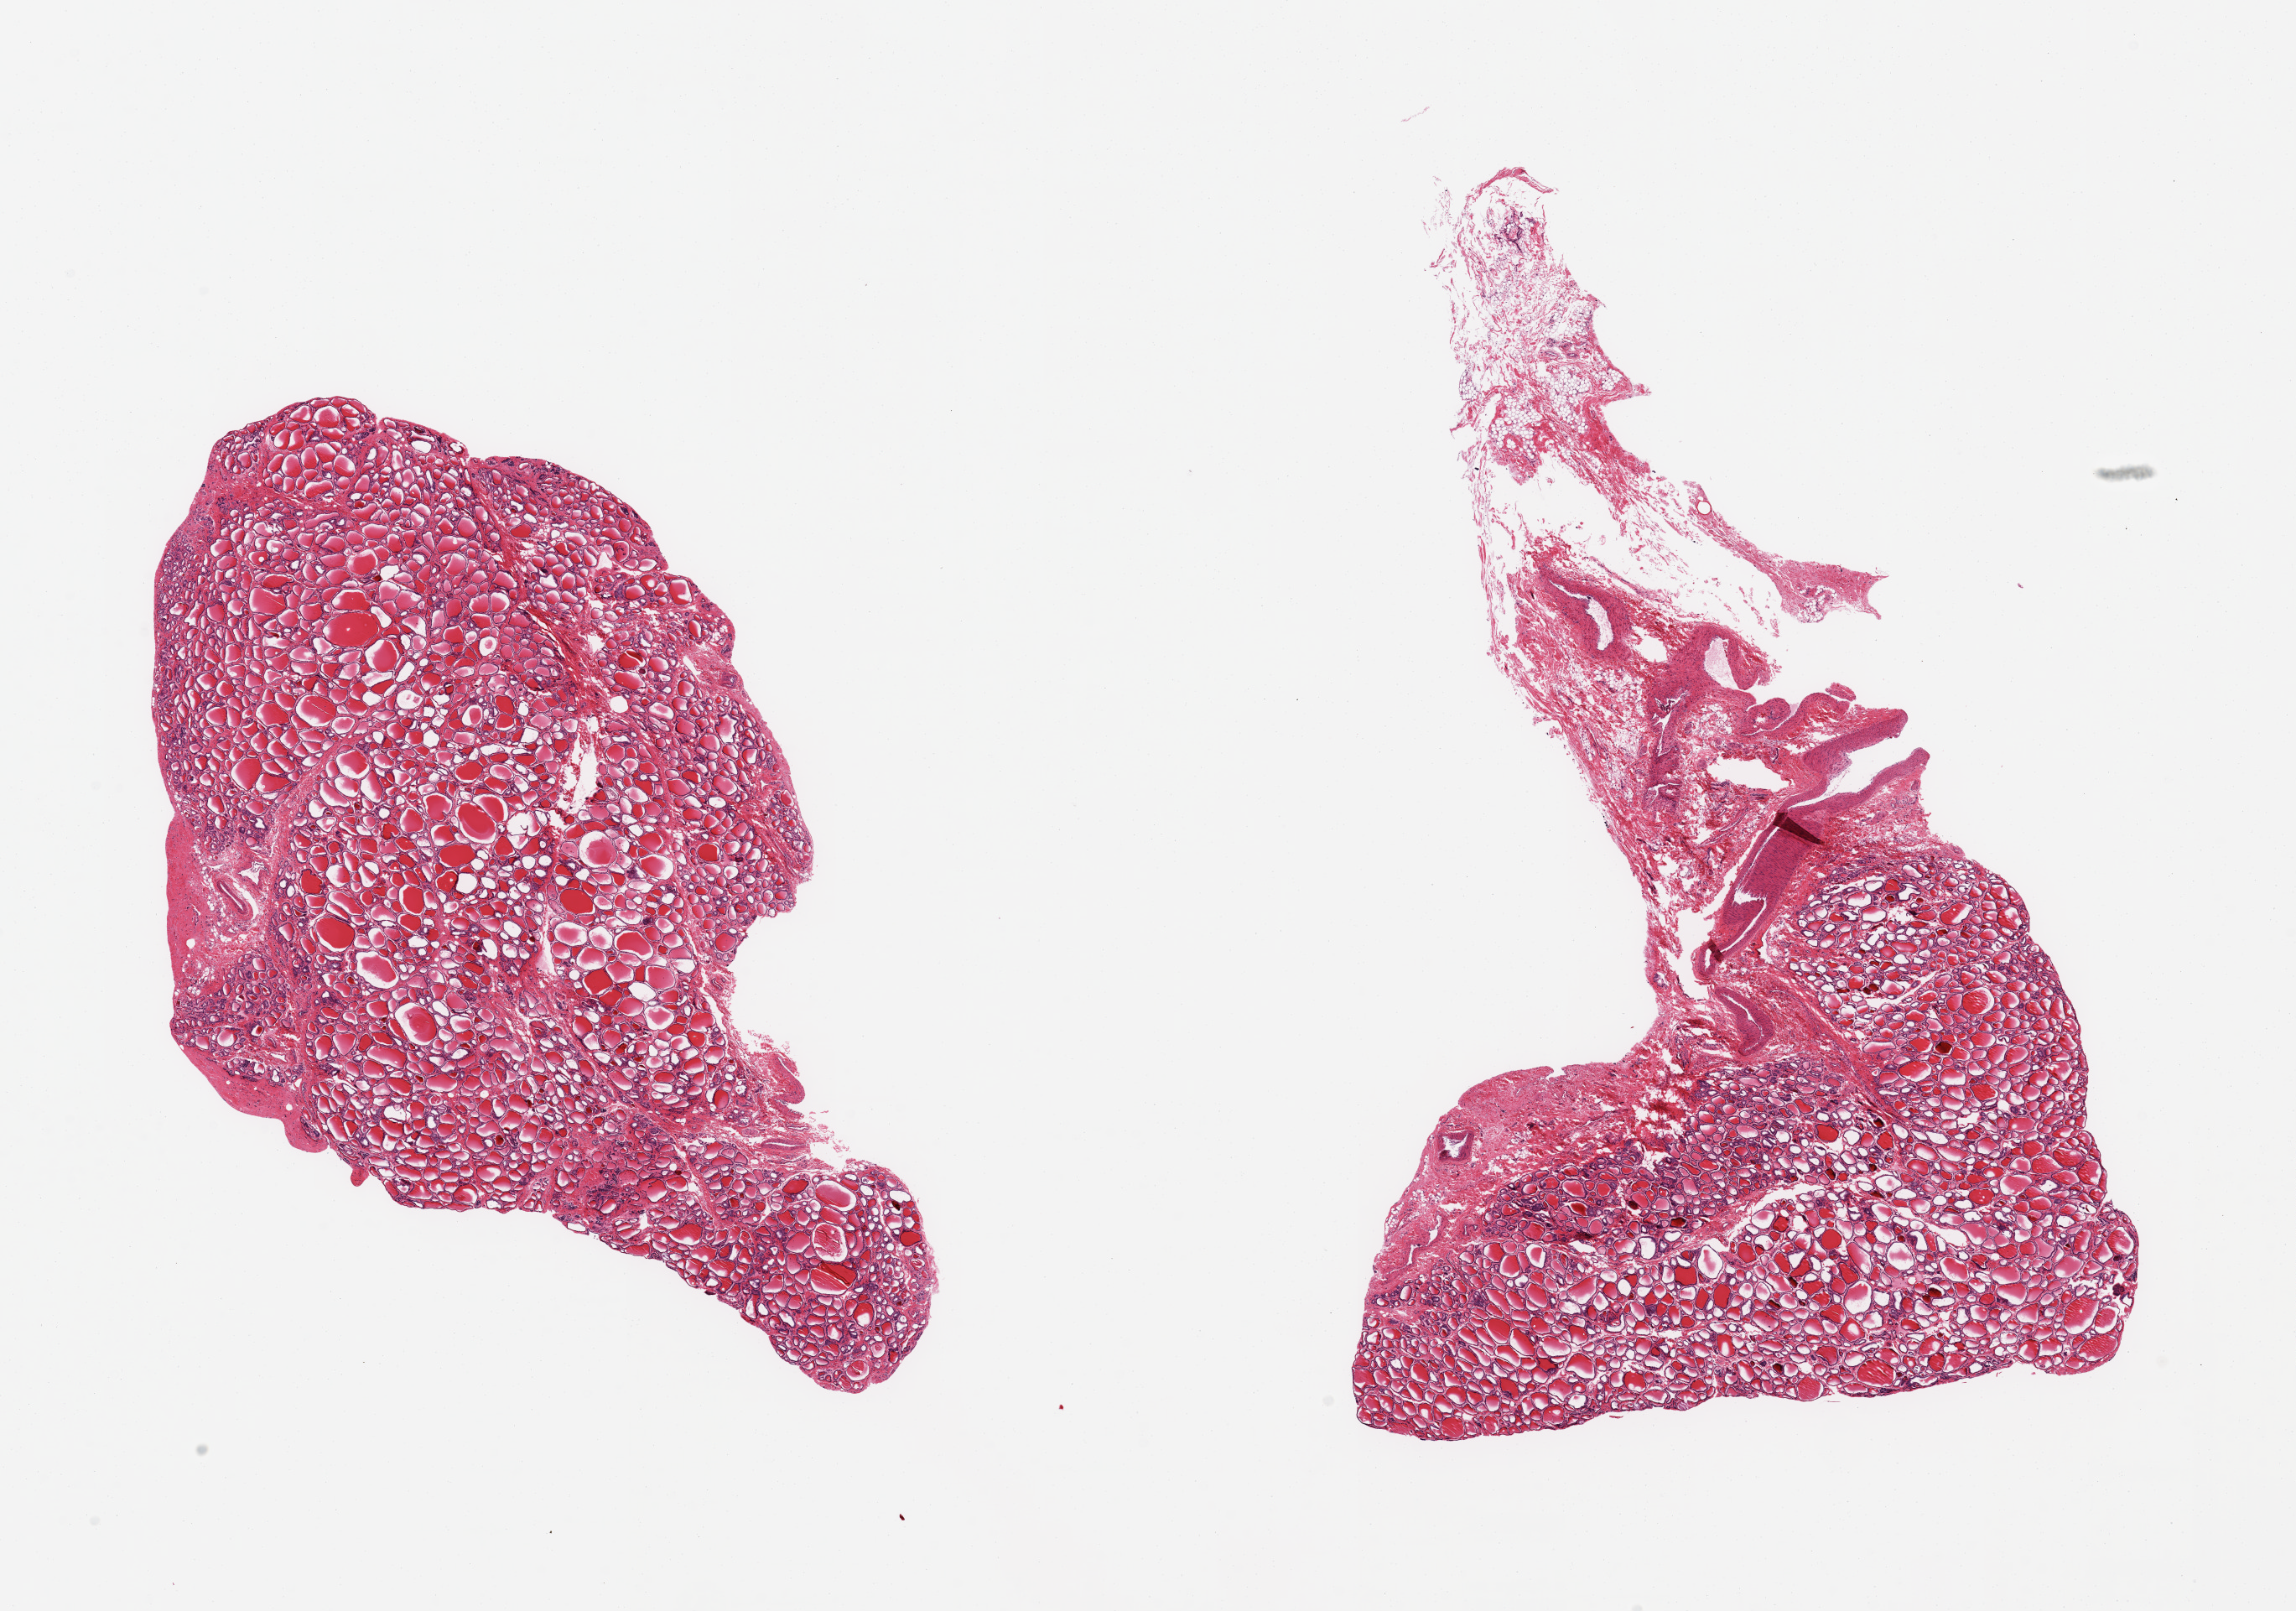
Whole-slide image, H&E stain, a low-resolution overview of the entire scanned area, about 21.7 x 15.2 mm (from a 20x scan), PAXgene-fixed, paraffin-embedded tissue, target tissue: thyroid, donor tissue sample. Male donor.
Pathologist's review note for this sample: 2 pieces, adherent fat/vascular elements on one edge, ~25% of specimen; sample carefully.